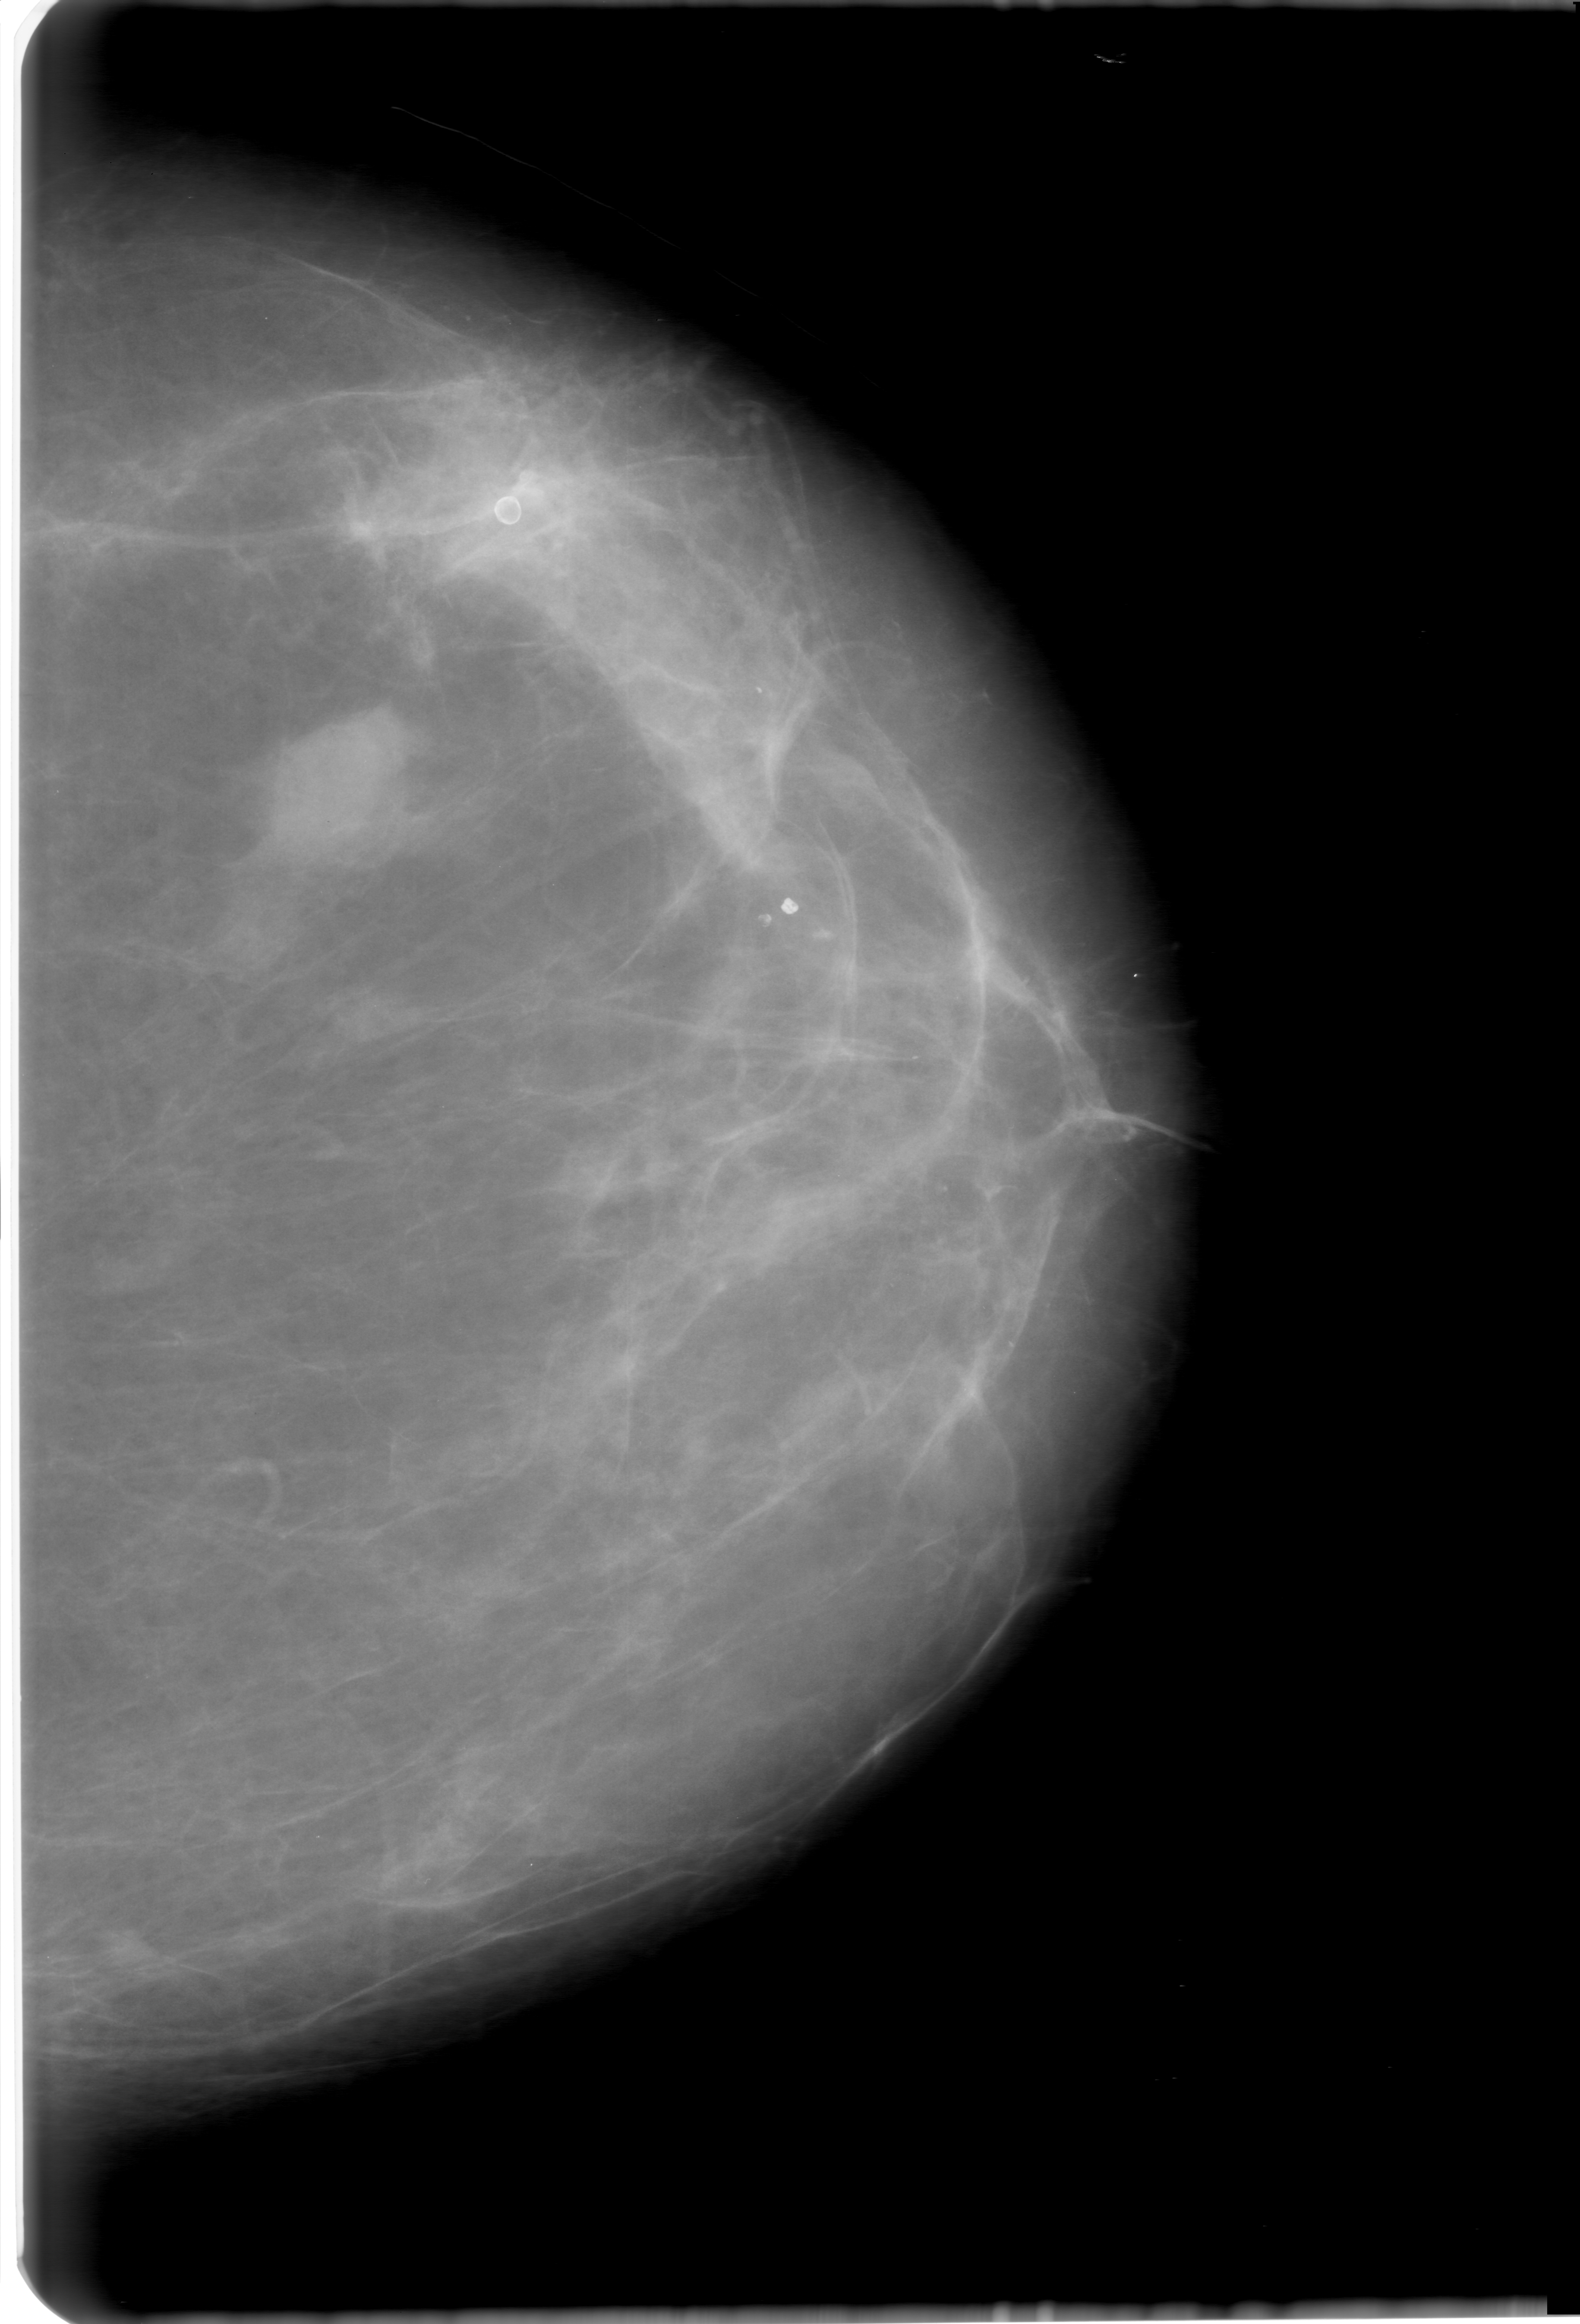
Digitized screen-film mammogram; left breast; craniocaudal (CC) view; BI-RADS breast density category 2 (scale 1–4); 1580 × 2324 image matrix.
Expert-marked regions of interest on this image (one box per marked abnormality):
- mass, shape oval, margins microlobulated; BI-RADS assessment category 0 (incomplete: needs additional imaging); subtlety rating 5 on a 1 (subtle) to 5 (obvious) scale; pathology result (as recorded, not read from the image): benign: box from (x=204, y=695) to (x=464, y=902) px